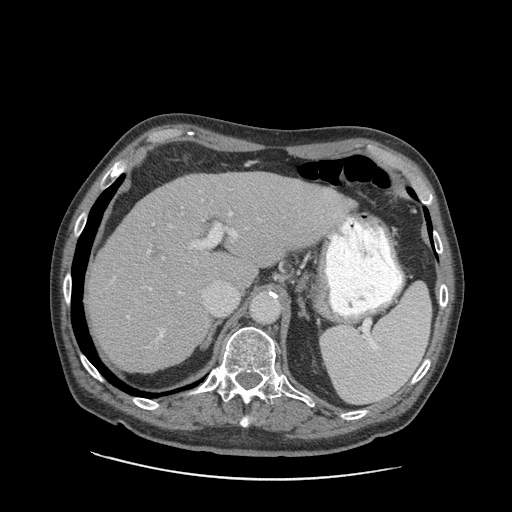
Contrast-enhanced abdominal CT (liver protocol), one axial slice; position 62 of 89 along the scan axis; 140 kVp; soft-tissue window (W 400 / L 40 HU); 2.5 mm slice thickness; 512 × 512 image matrix, field of view 420 × 420 mm. Case-level facts recorded for this patient, not image findings: diagnosis: hepatocellular carcinoma (patient treated with transarterial chemoembolisation; whether this scan precedes or follows treatment is not stated here); TNM stage (as recorded): Stage-I; Child-Pugh class: A; tumour differentiation: moderately differentiated; tumour nodularity: uninodular.
Annotated regions visible in this slice (semi-automatic segmentation, software-assisted and operator-edited):
- liver parenchyma outside the tumour (the mass and vessels are separate outlines, so this box may not span the whole liver): box from (x=88, y=172) to (x=352, y=372) px
- liver vessels: (x=110, y=190)–(x=343, y=348)